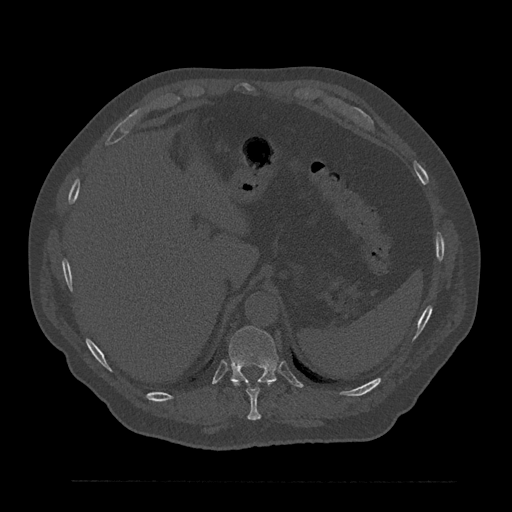
CT including the spine, one axial slice. Bone window (W 1800 / L 400 HU). 512 × 512 image matrix. Male patient, age 61 years. From the clinical record (not read from this slice): primary cancer: prostate.
Outlined on this slice (semi-automatically segmented with operator editing):
- T10 vertebra: bounding box (x1, y1, x2, y2) in pixels: (231, 380, 272, 421)
- T11 vertebra: (229, 326, 278, 385)